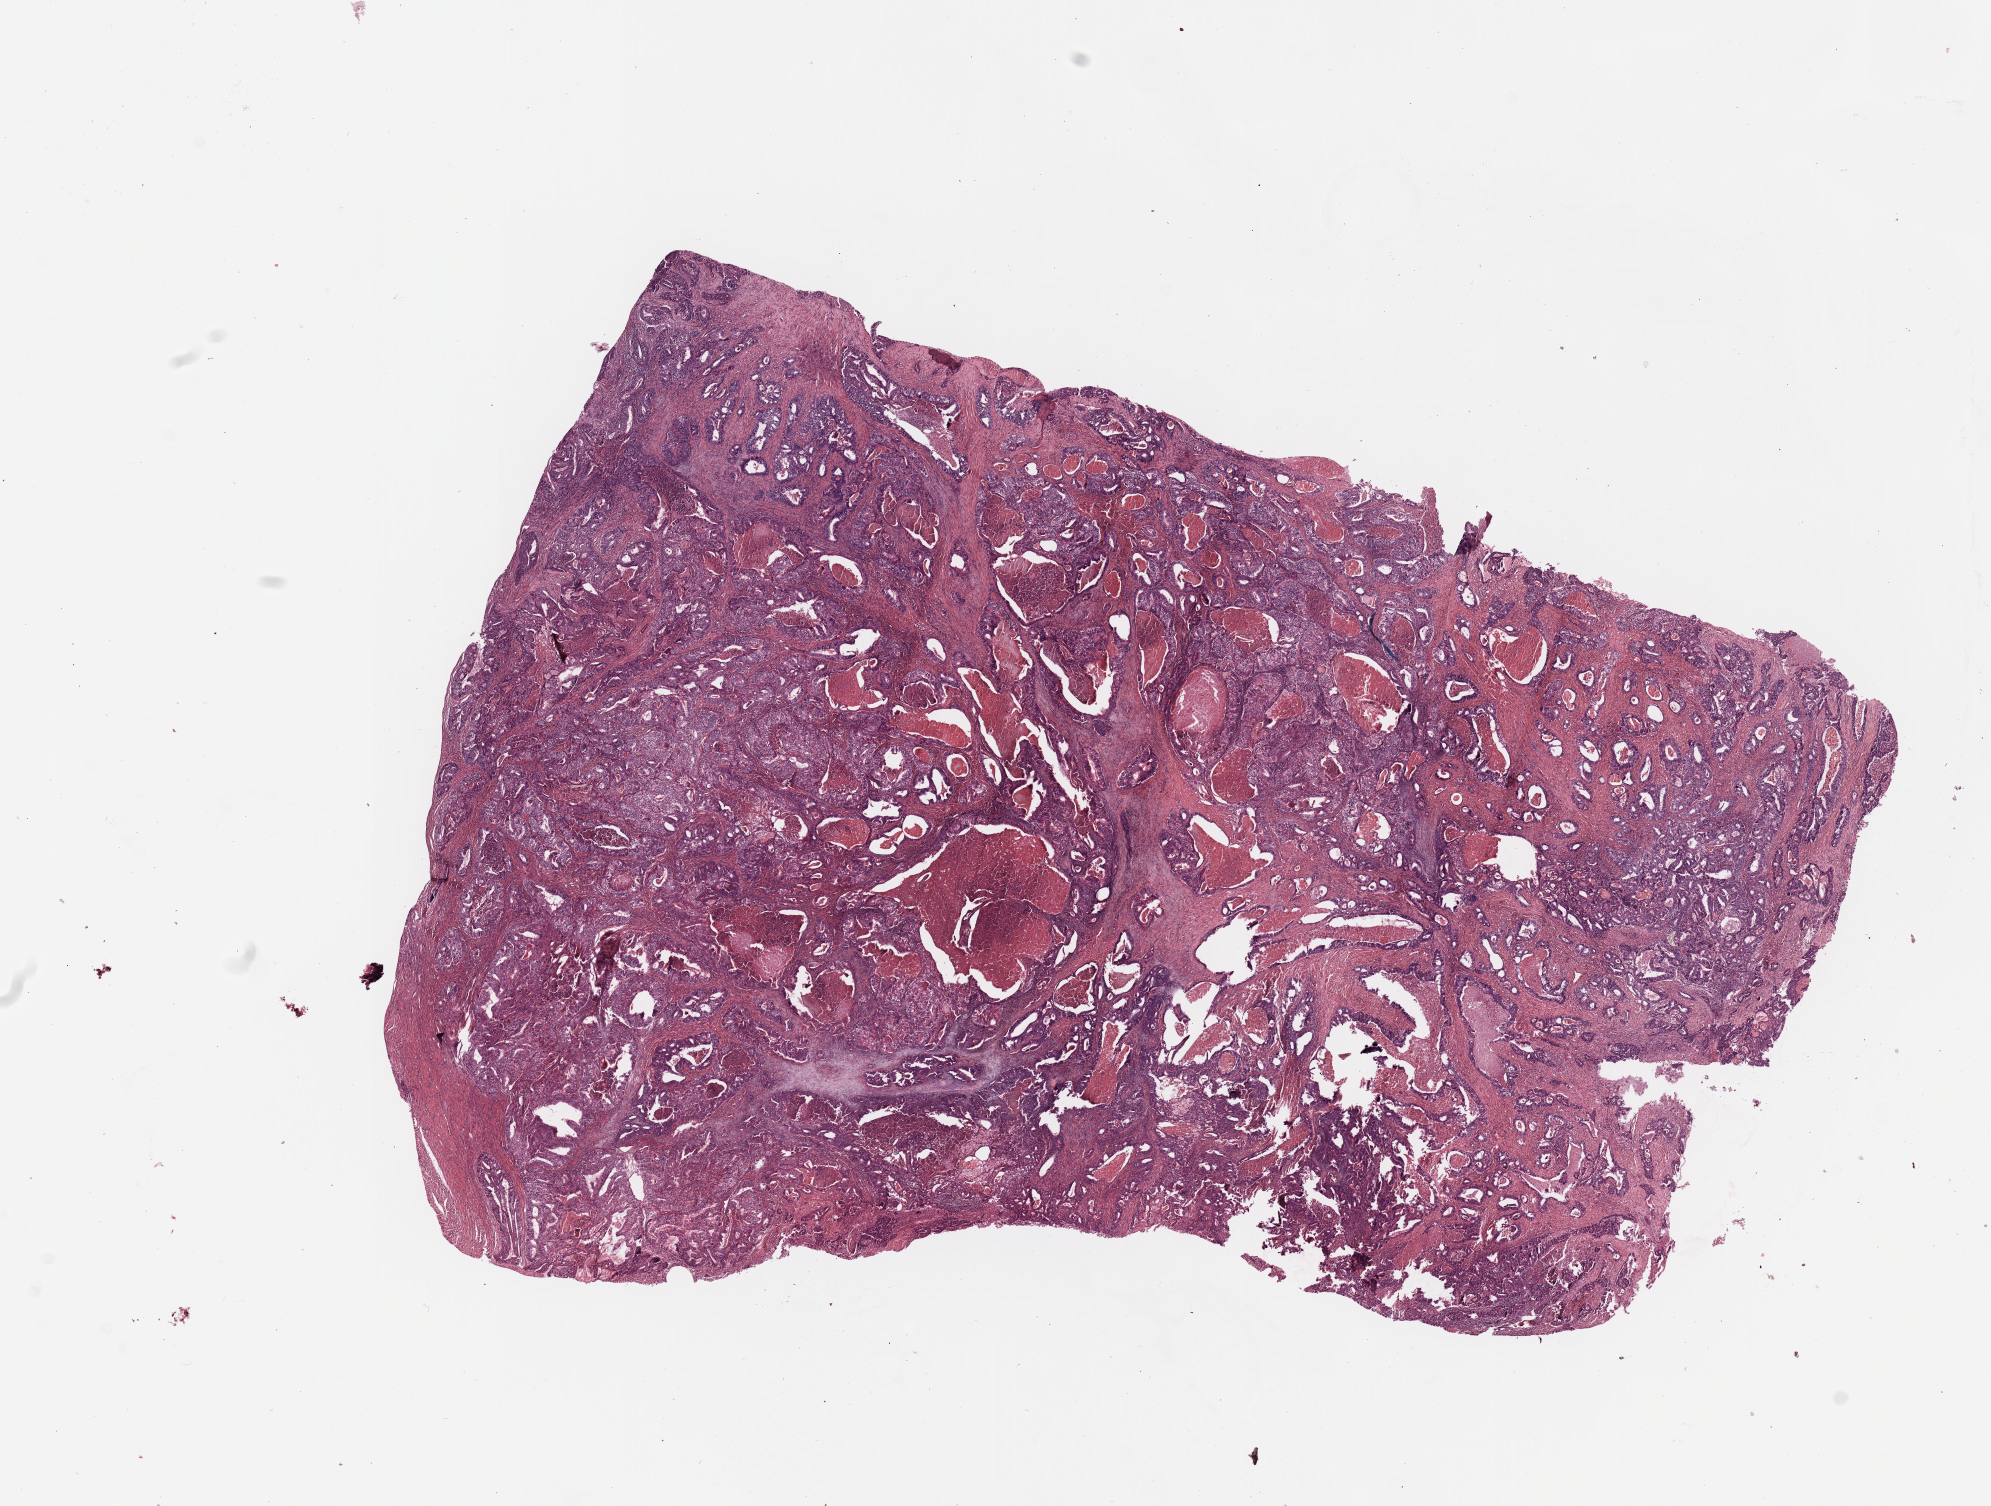
Hematoxylin and eosin (H&E) stained whole-slide image — a low-resolution overview of the entire scanned area, about 15.8 x 11.9 mm (slide scanned at 20x), tumour tissue sample, uterus. 68-year-old female patient. Histologic grade: G2 (moderately differentiated).
AJCC pathologic stage: I. Diagnosis: Endometrioid adenocarcinoma, NOS.